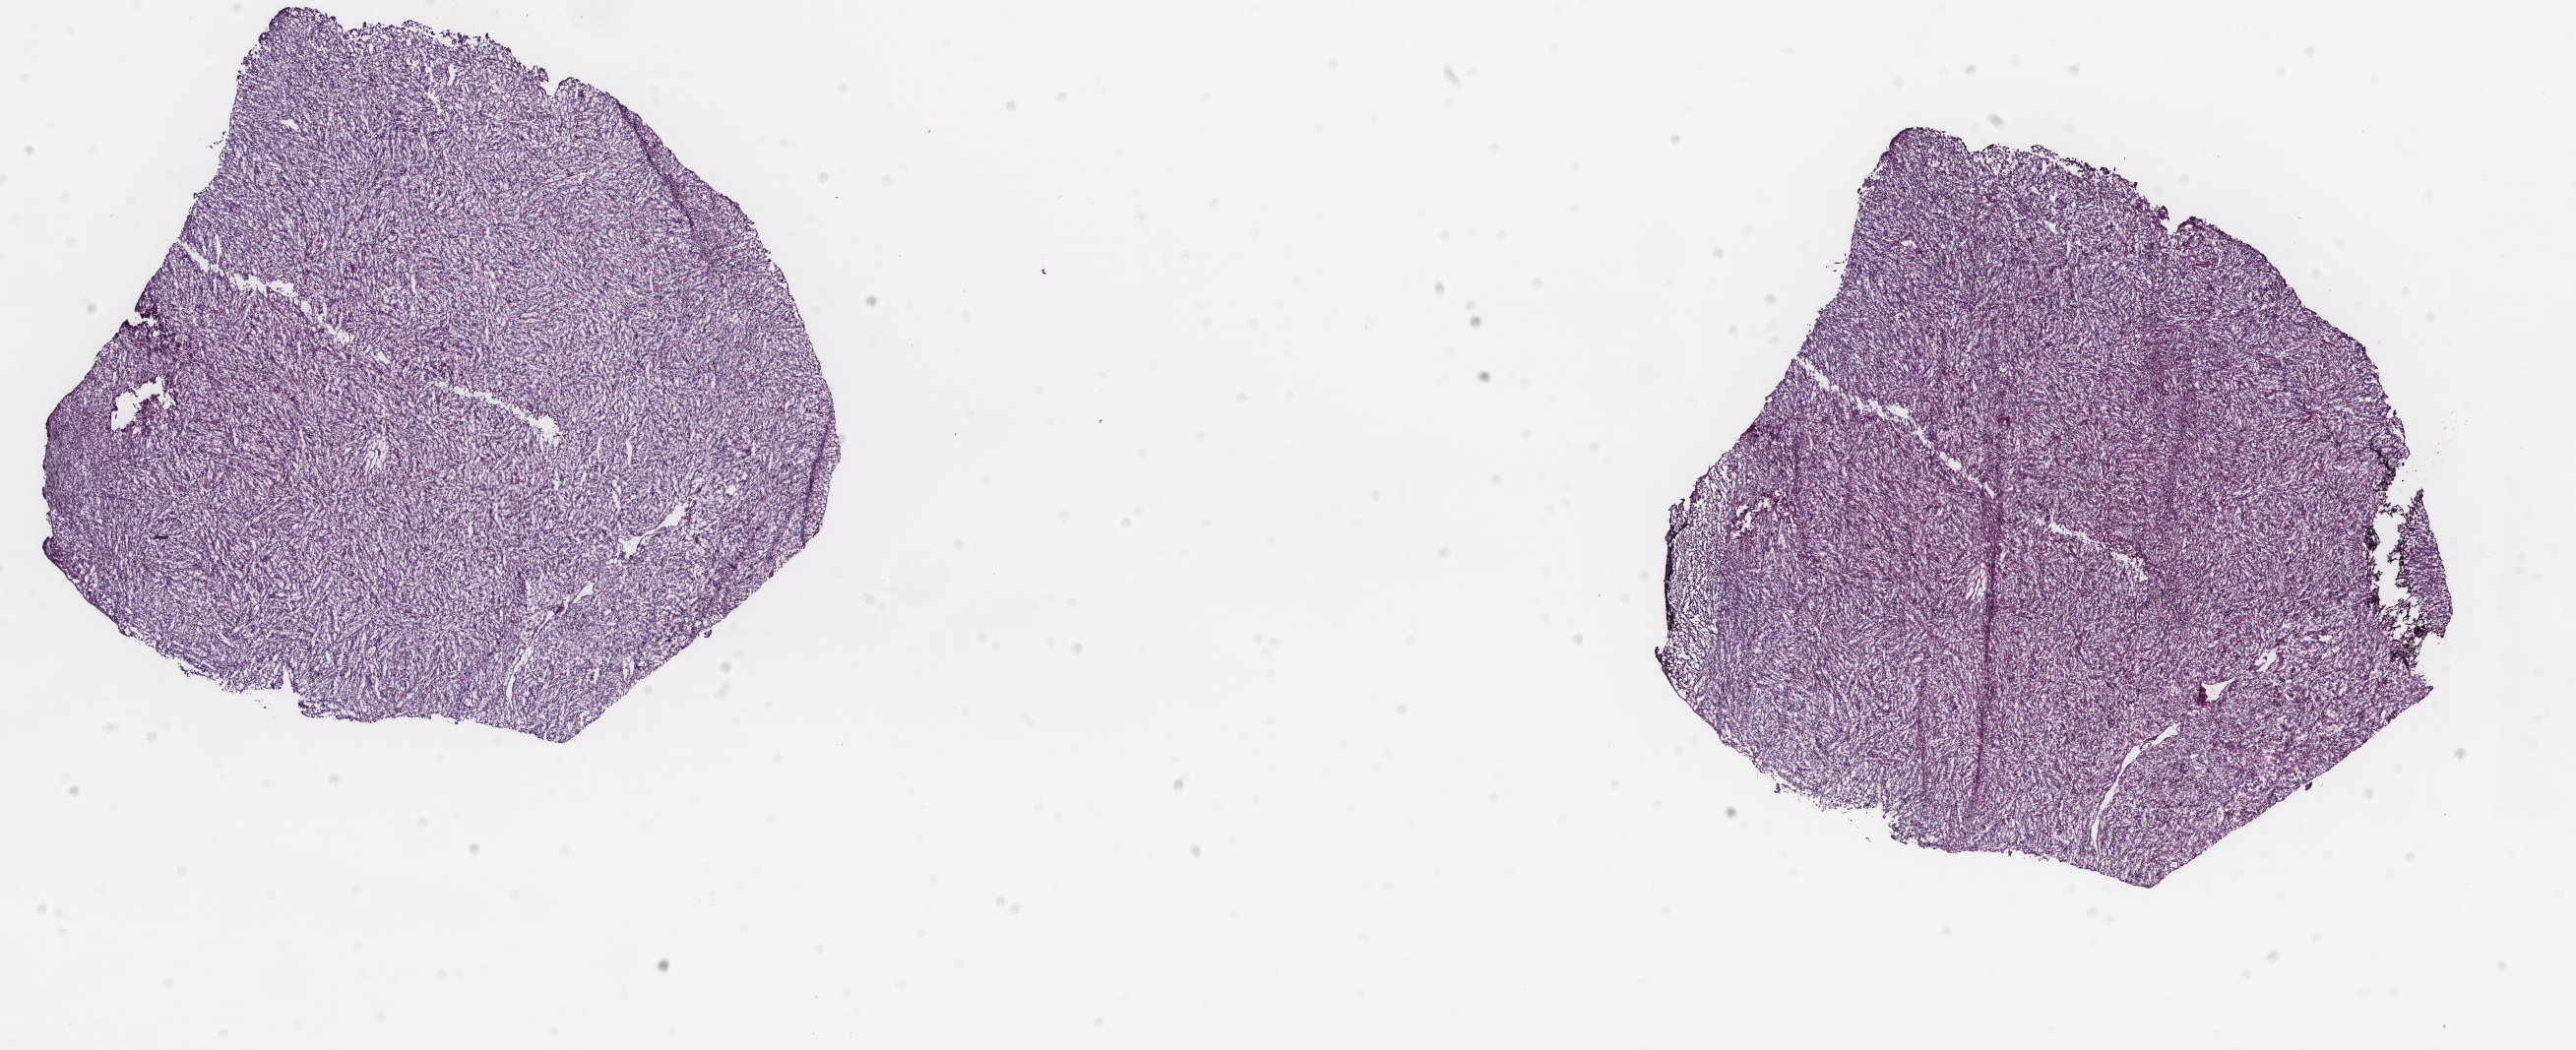
Hematoxylin and eosin (H&E) stained whole-slide image, a low-resolution overview of the entire scanned area, about 20.8 x 8.5 mm; frozen section from the top of the tissue portion; metastatic tumour sample. Patient: male, age at initial diagnosis 40 years. Slide review estimates, as recorded: tumour cells 85%, tumour nuclei 85%, normal cells 0%, stromal cells 14%, necrosis 1%. Inflammatory infiltration, as recorded: lymphocyte infiltration 2%, monocyte infiltration 1%, neutrophil infiltration 0%.
- this section: metastatic tumour tissue
- patient diagnosis: Malignant melanoma, NOS